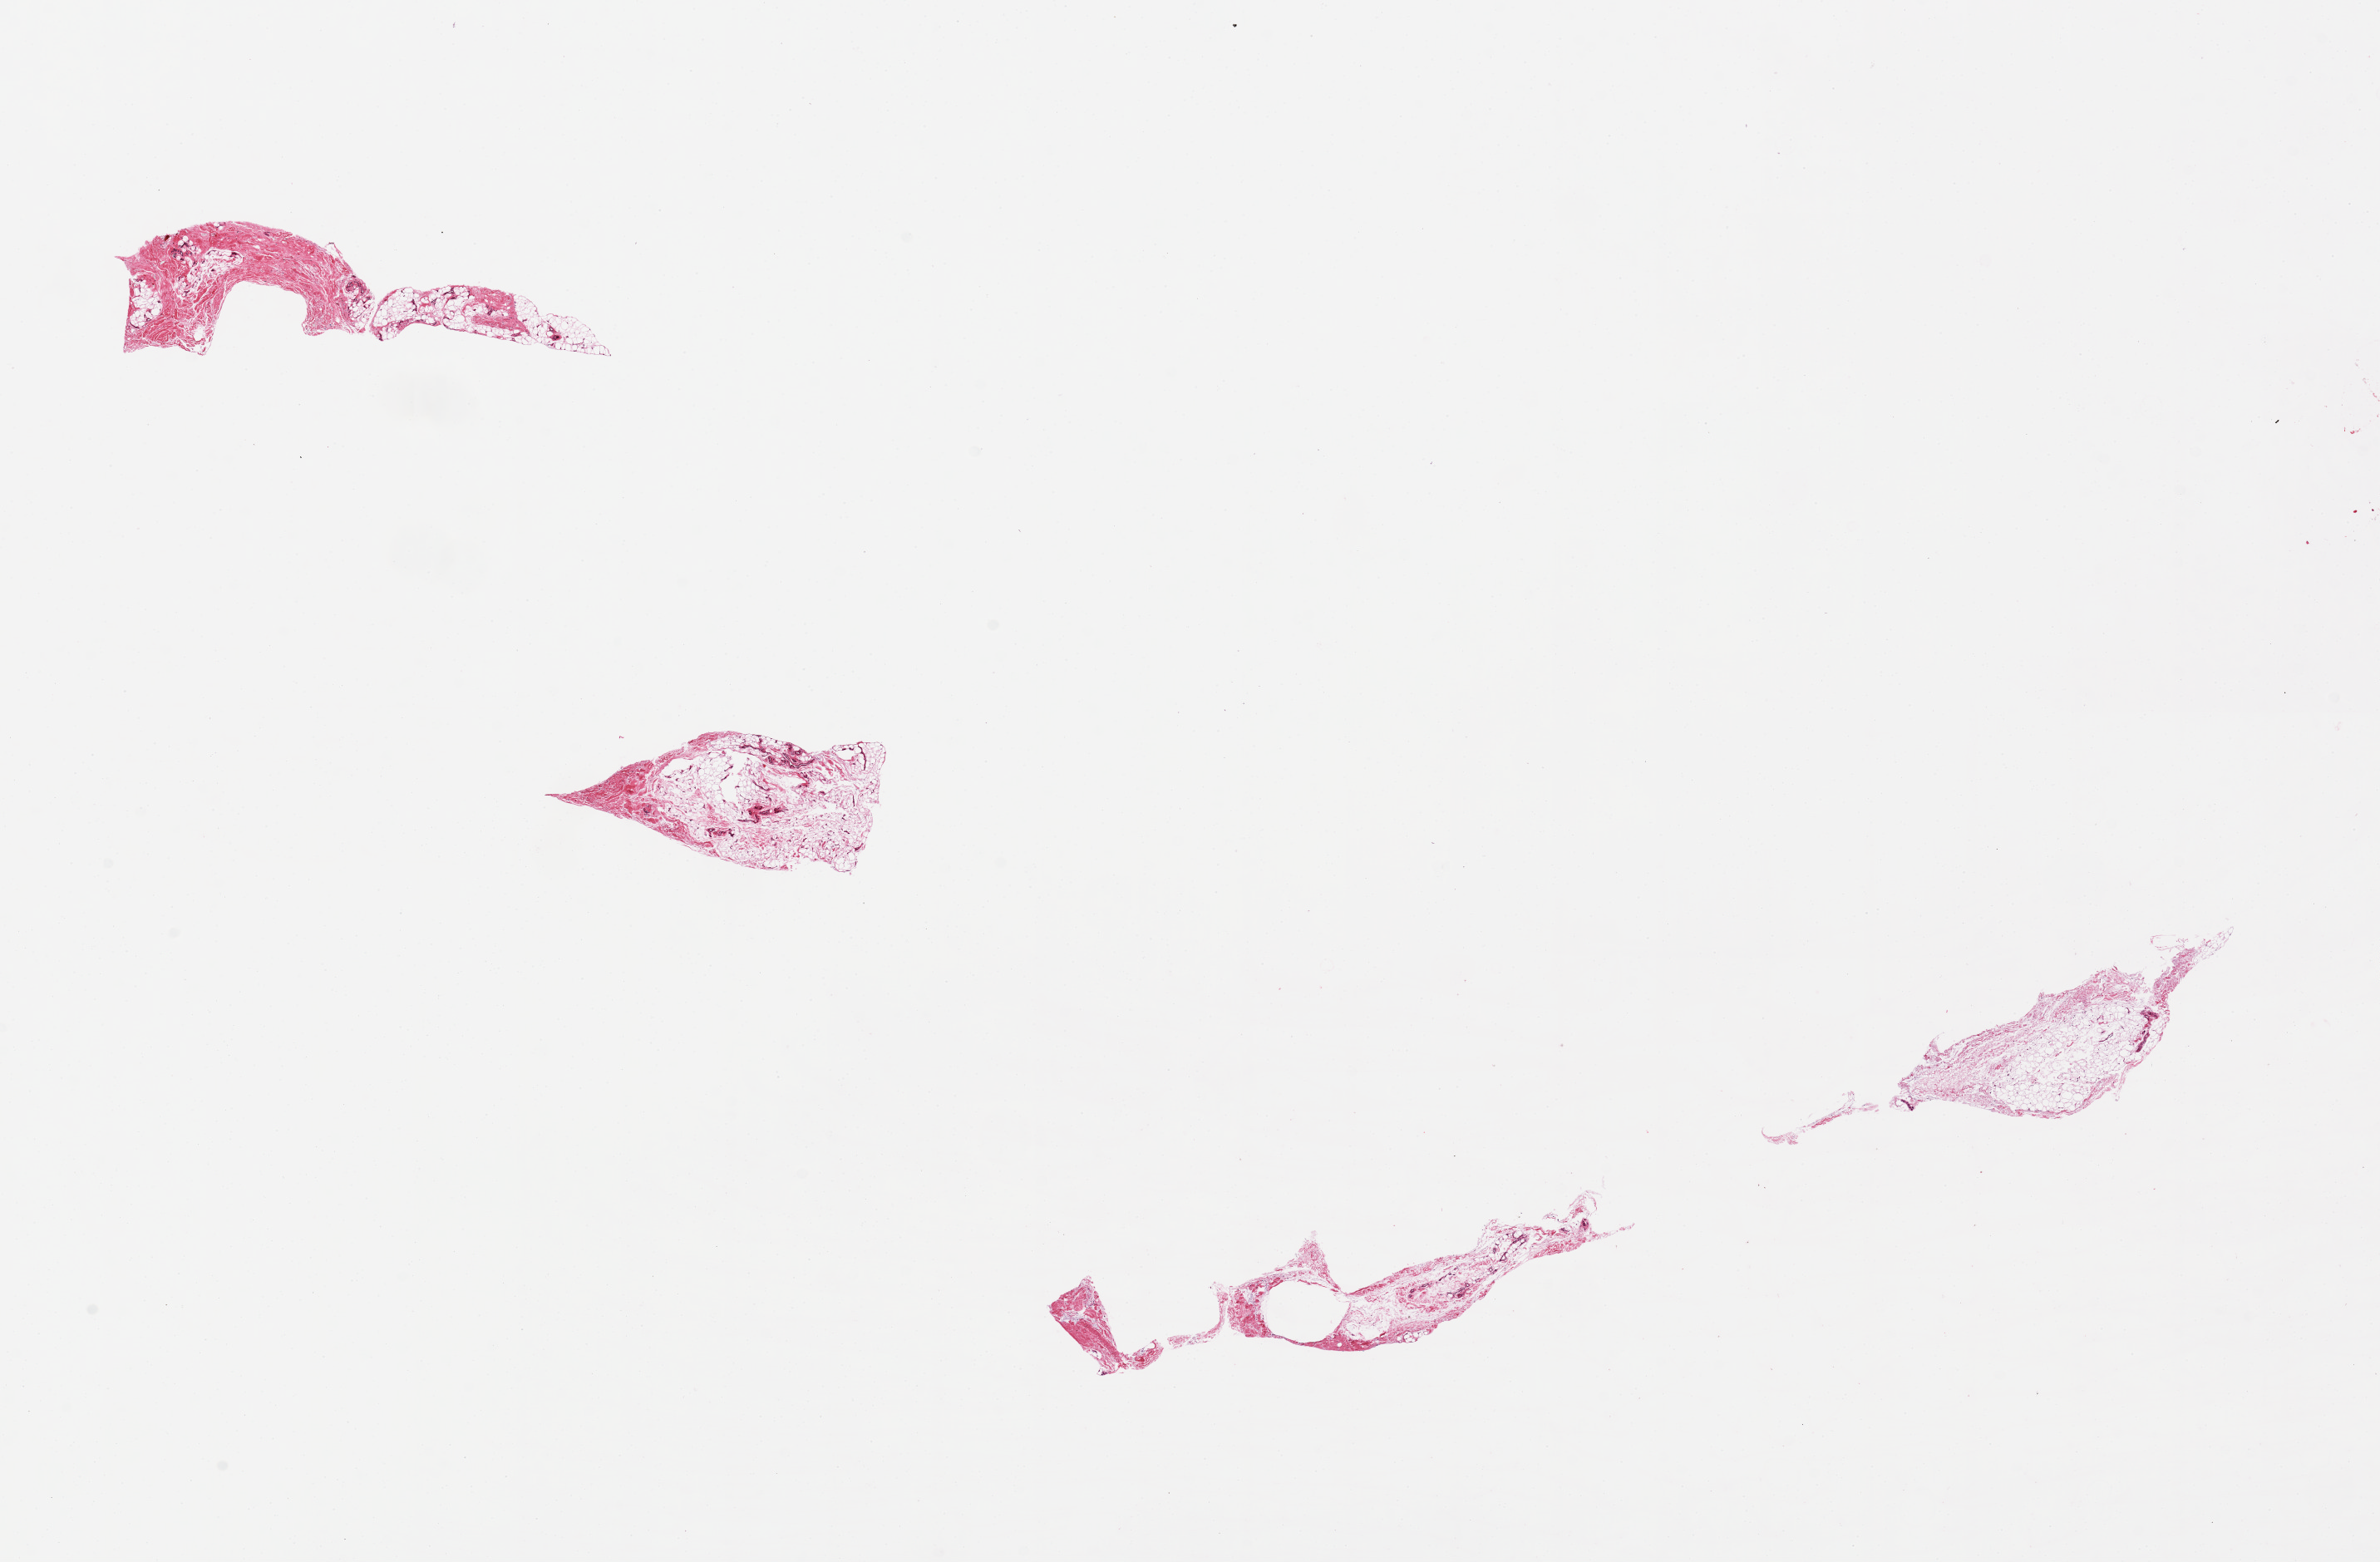
Digitized haematoxylin and eosin-stained section — whole scanned area (about 22.6 x 14.9 mm) shown as a low-resolution overview; PAXgene-fixed, paraffin-embedded tissue; sampled site (target tissue): tibial artery; donor tissue sample. Donor sex: male.
Review note (as recorded): Trace shreds of fibroadipose tissue; no artery present.